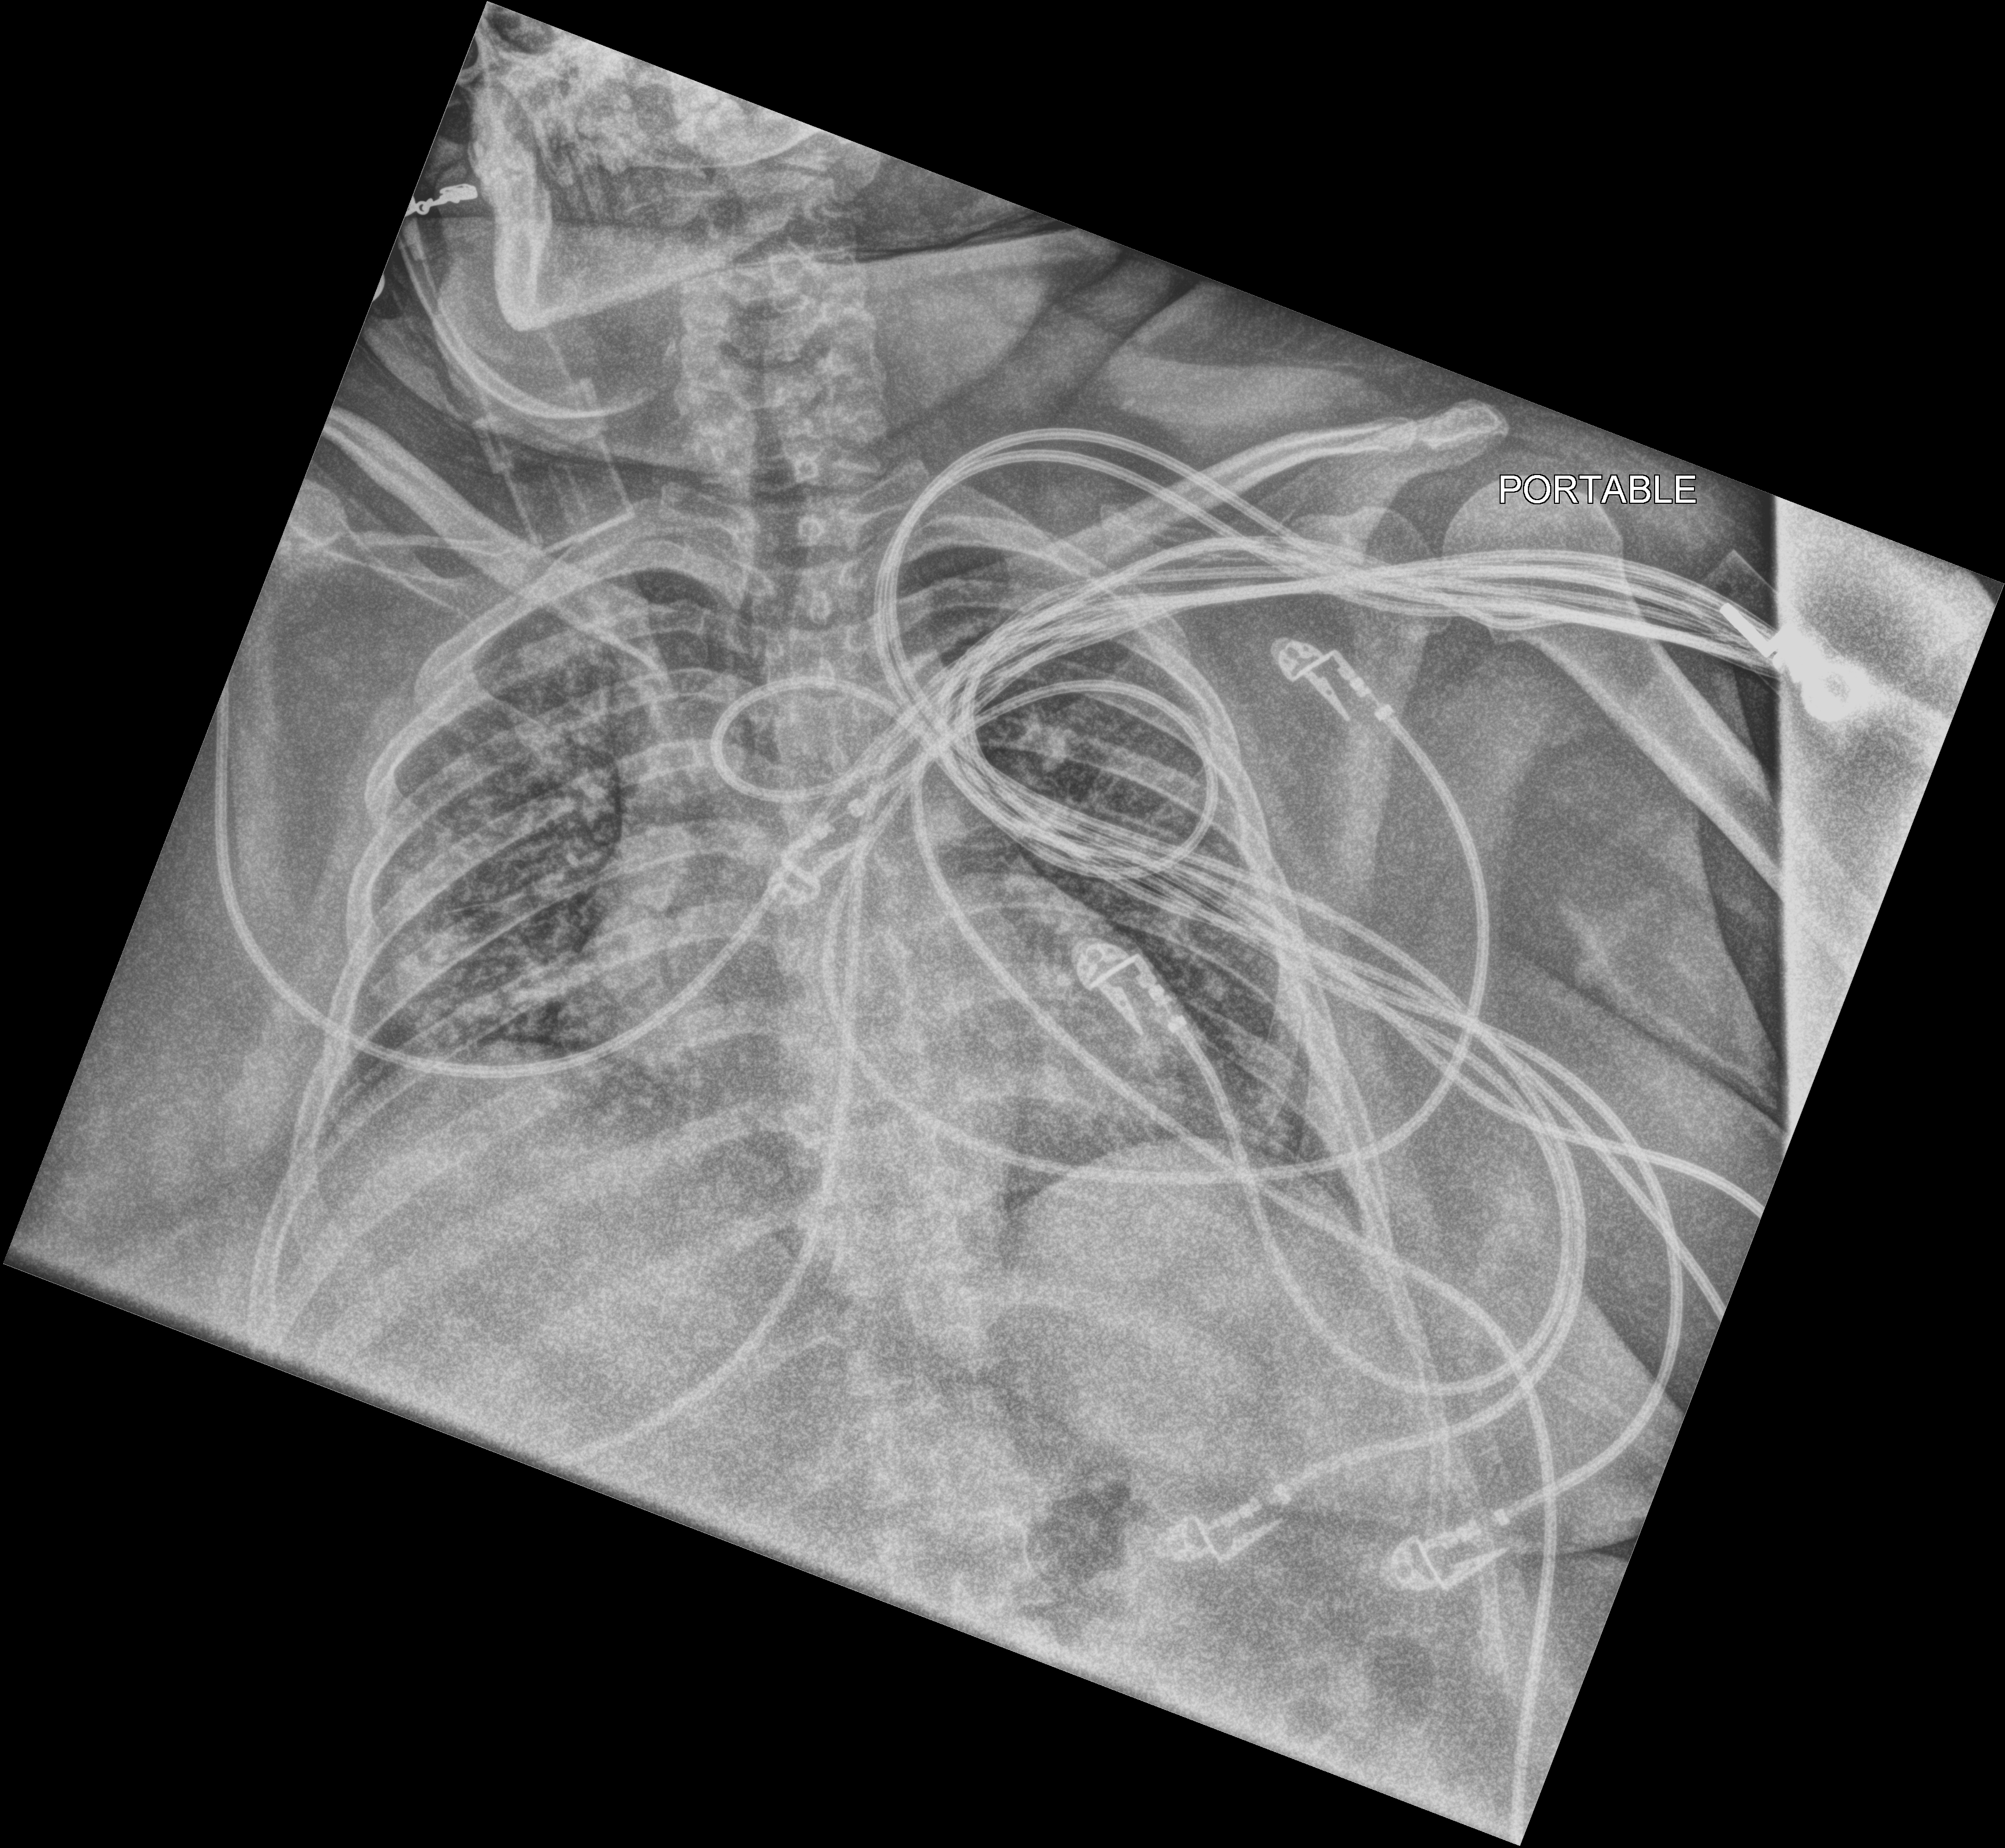
Portable chest radiograph. Patient hospitalised with COVID-19; female, aged 18–59 years.
From the hospital-stay record, not from the radiograph (when in the stay this image was taken is not recorded):
- chronic kidney disease (admission record): no